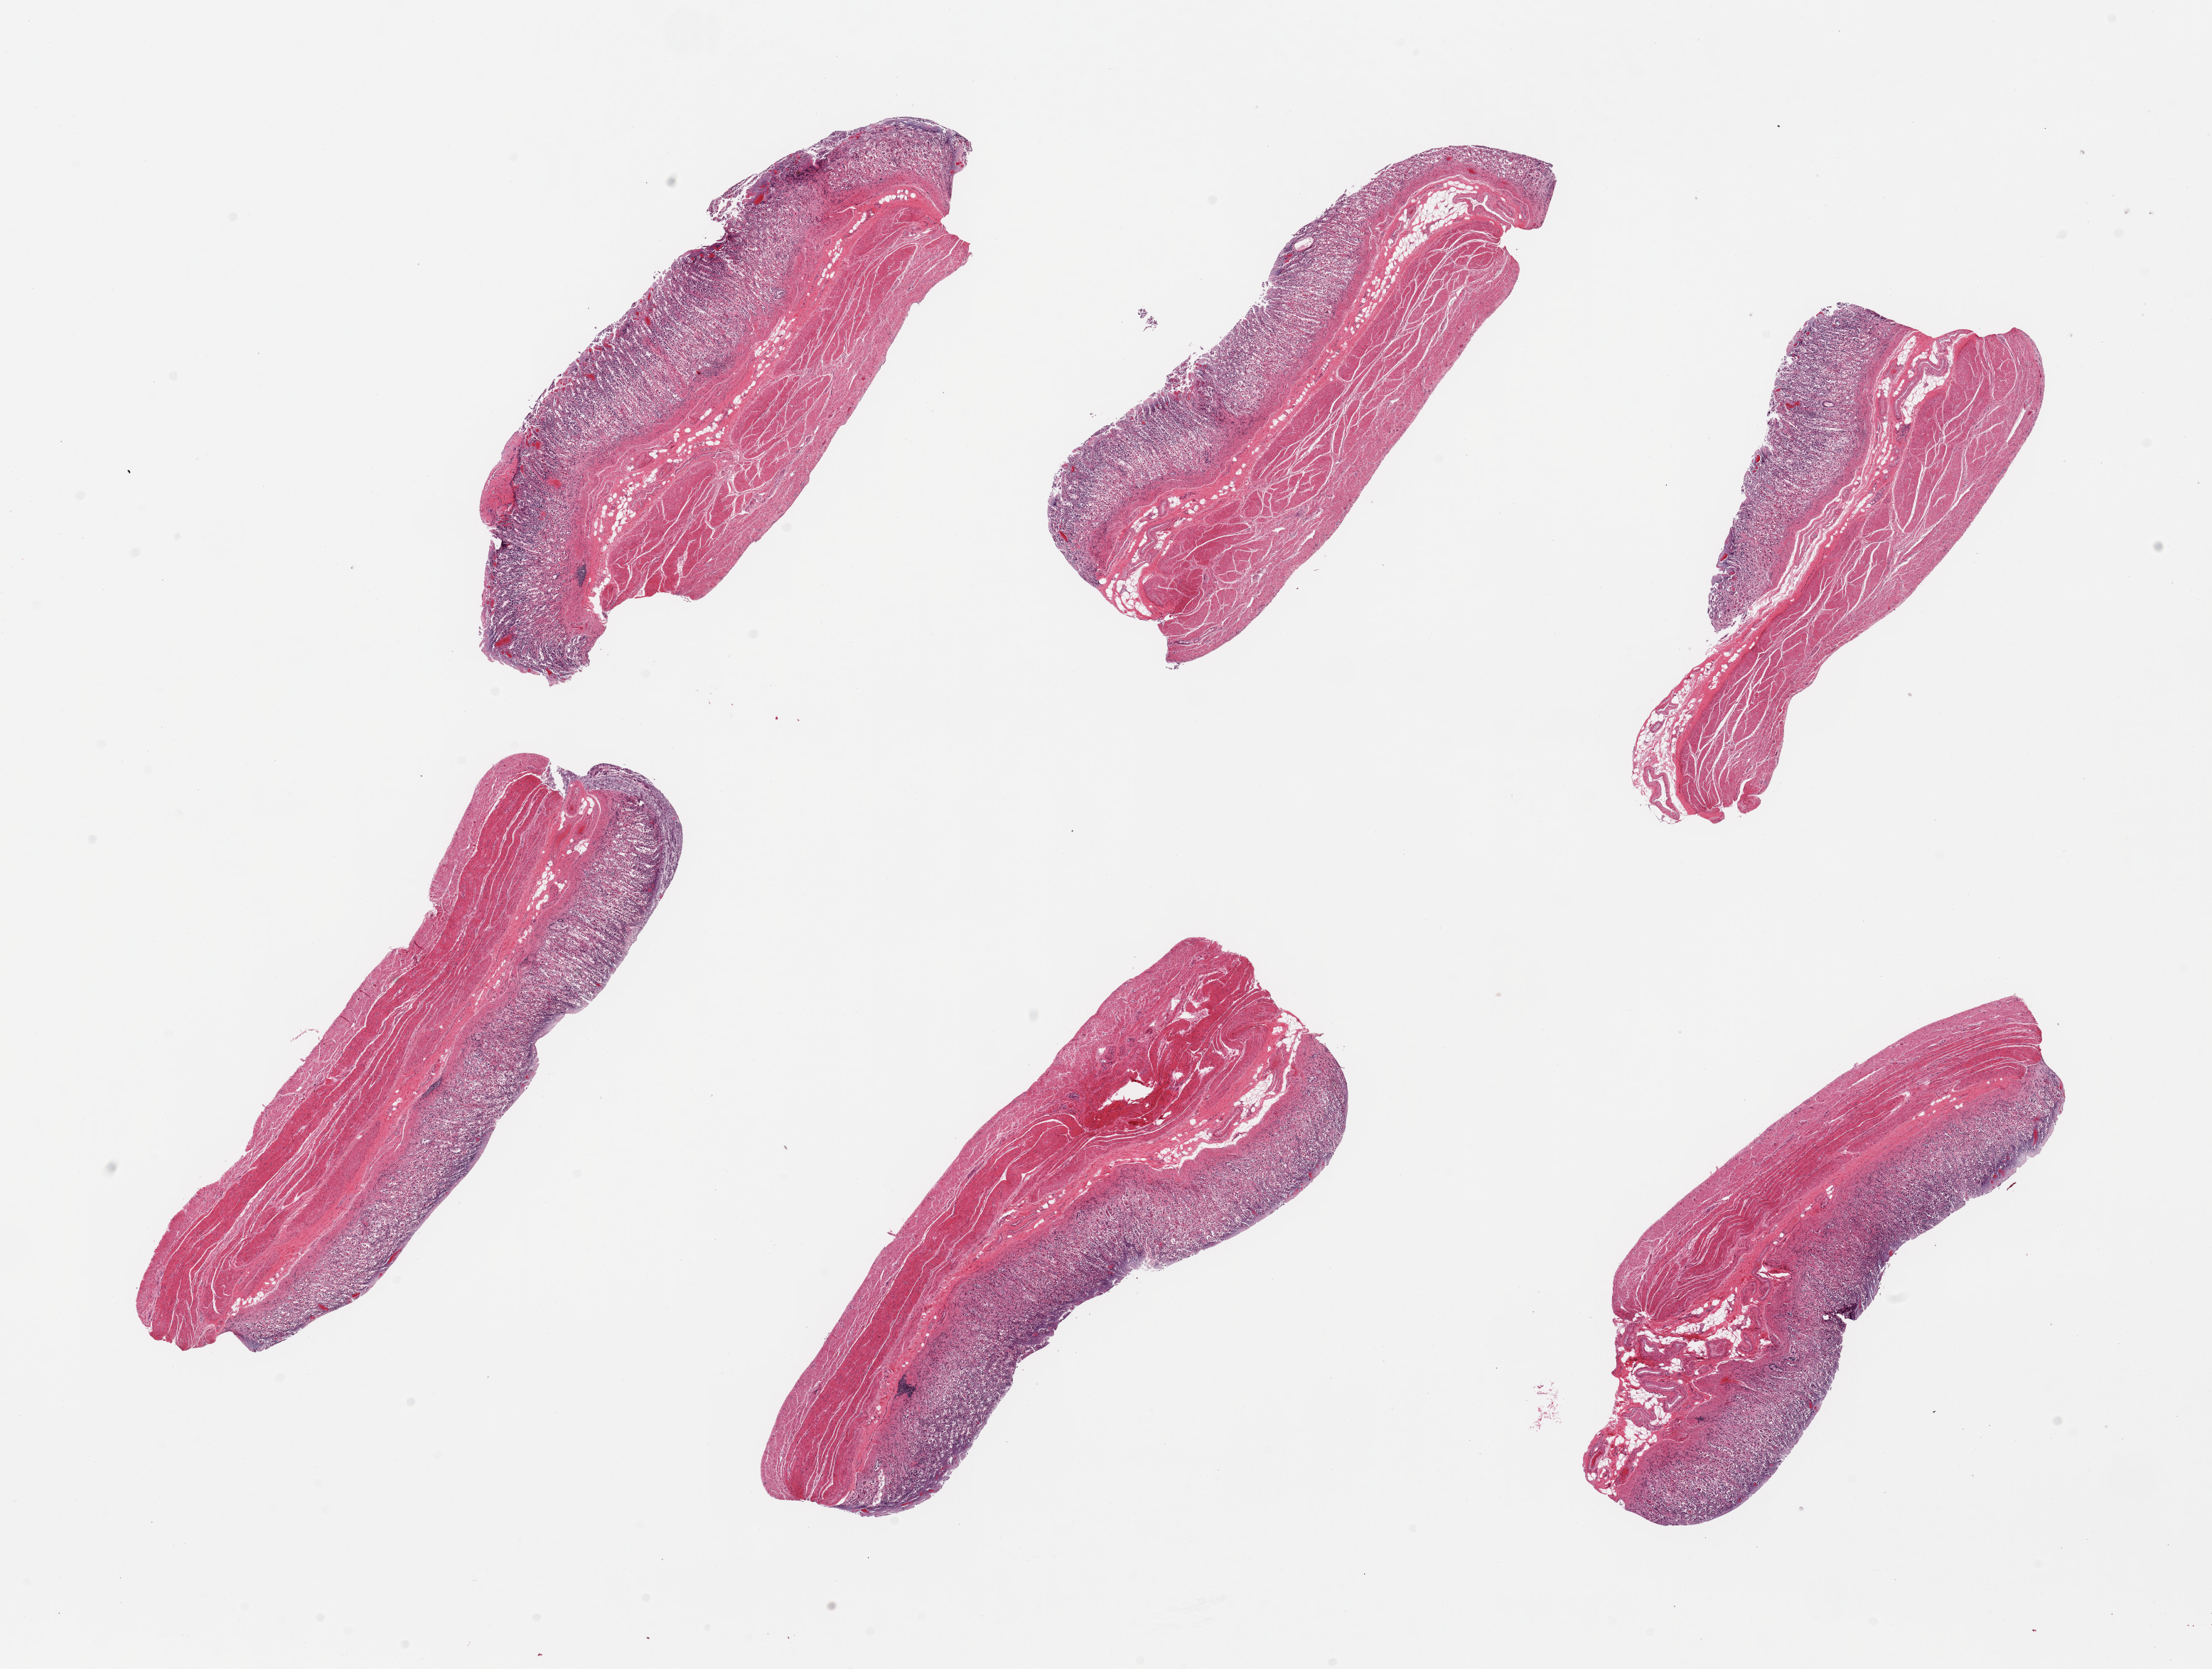
Whole-slide image, haematoxylin and eosin stain, whole scanned area (about 24.6 x 18.6 mm) shown as a low-resolution overview, PAXgene-fixed, paraffin-embedded tissue, sampled site (target tissue): stomach, tissue donor sample. Donor sex: male.
• pathologist's review note for this sample: 6 pieces; full thickness sections (mucosa is moderately to severely autolyzed, muscularis moderately autolyzed)